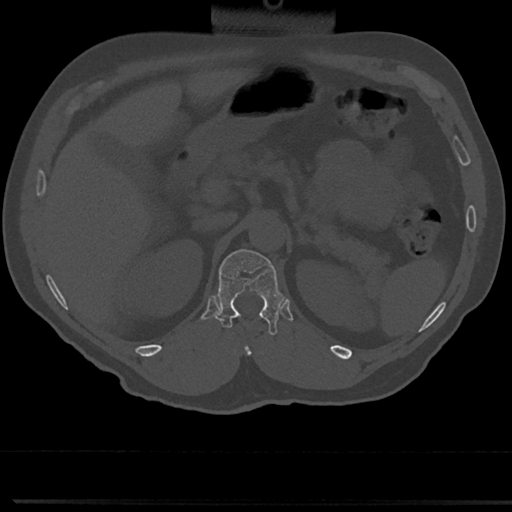
CT including the spine, one axial slice; position 153 of 817 along the scan axis; 120 kVp; bone window (W 1800 / L 400 HU); 0.5 mm slice thickness; 512 × 512 image matrix, field of view 355 × 355 mm. Patient: male, 61 years. Case-level facts recorded for this patient, not image findings: primary cancer: prostate.
Annotated regions visible in this slice (semi-automatic segmentation, software-assisted and operator-edited):
- T12 vertebra: bounding box <214,246,280,333> (left, top, right, bottom; pixels)